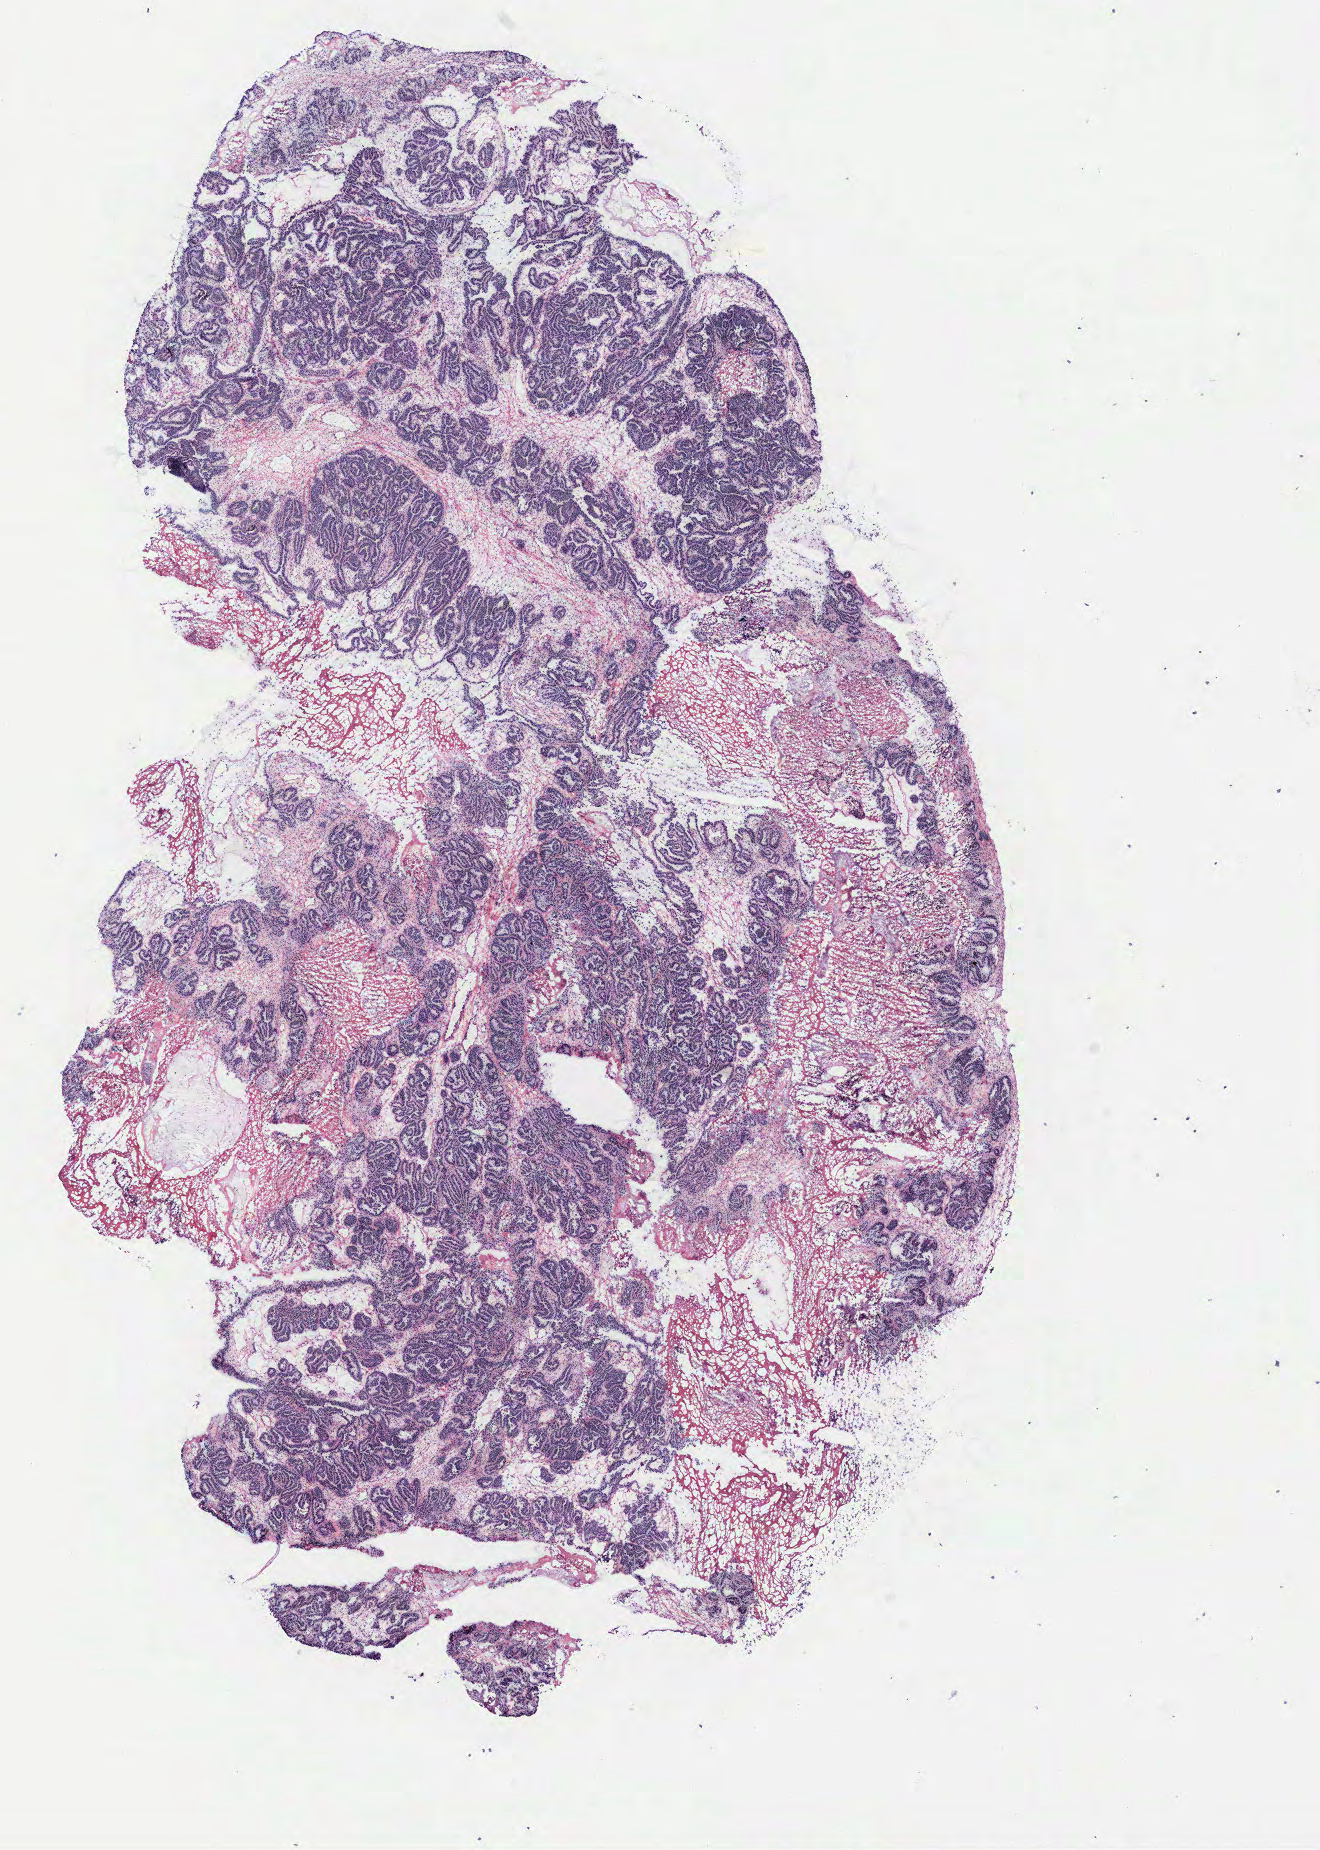
H&E-stained whole-slide image, low-resolution overview of the scanned area, about 10.6 x 14.8 mm (from a 40x scan); ovary, tumour tissue. 55-year-old female patient.
Diagnosis: Serous adenocarcinoma, NOS (fallopian tube).